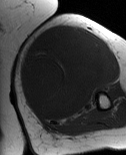
MRI of an extremity soft-tissue mass, one axial slice; position 41 of 86 along the scan axis; MR volume resampled by the dataset authors to the PET/CT grid (not the native acquisition matrix); 3.27 mm slice thickness; 126 × 155 image matrix. Female patient. Case-level facts recorded for this patient, not image findings: histological type: pleiomorphic leiomyosarcoma; grade: high; site of the primary tumour: left biceps.
Annotated regions visible in this slice (expert contour drawn on MRI and transferred to this co-registered scan by the dataset authors):
- gross tumour volume including surrounding oedema: bounding box [x1, y1, x2, y2] px = [20, 26, 108, 121]
- gross tumour volume (mass): [20, 26, 108, 119]